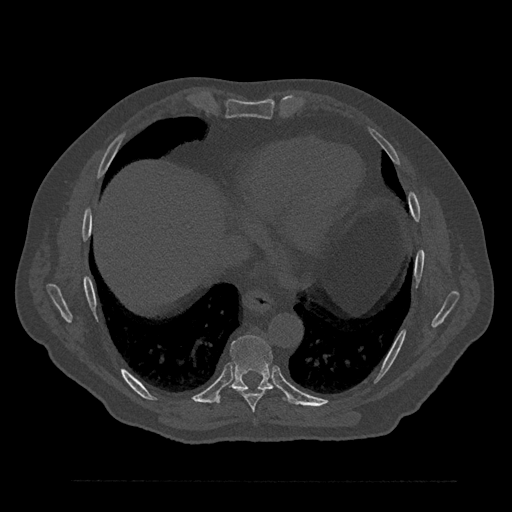
CT including the spine, one axial slice; slice 430 of 797 in the series (ordered by position); reconstruction kernel Br40s/3; 120 kVp; bone window (W 1800 / L 400 HU); 0.5 mm slice thickness; 512 × 512 image matrix, field of view 430 × 430 mm. Male patient, age 61 years. From the clinical record (not read from this slice): primary cancer: prostate.
Outlined on this slice (semi-automatic segmentation, software-assisted and operator-edited):
- T8 vertebra: bounding box [x1, y1, x2, y2] px = [236, 388, 269, 412]
- T9 vertebra: [215, 335, 291, 405]